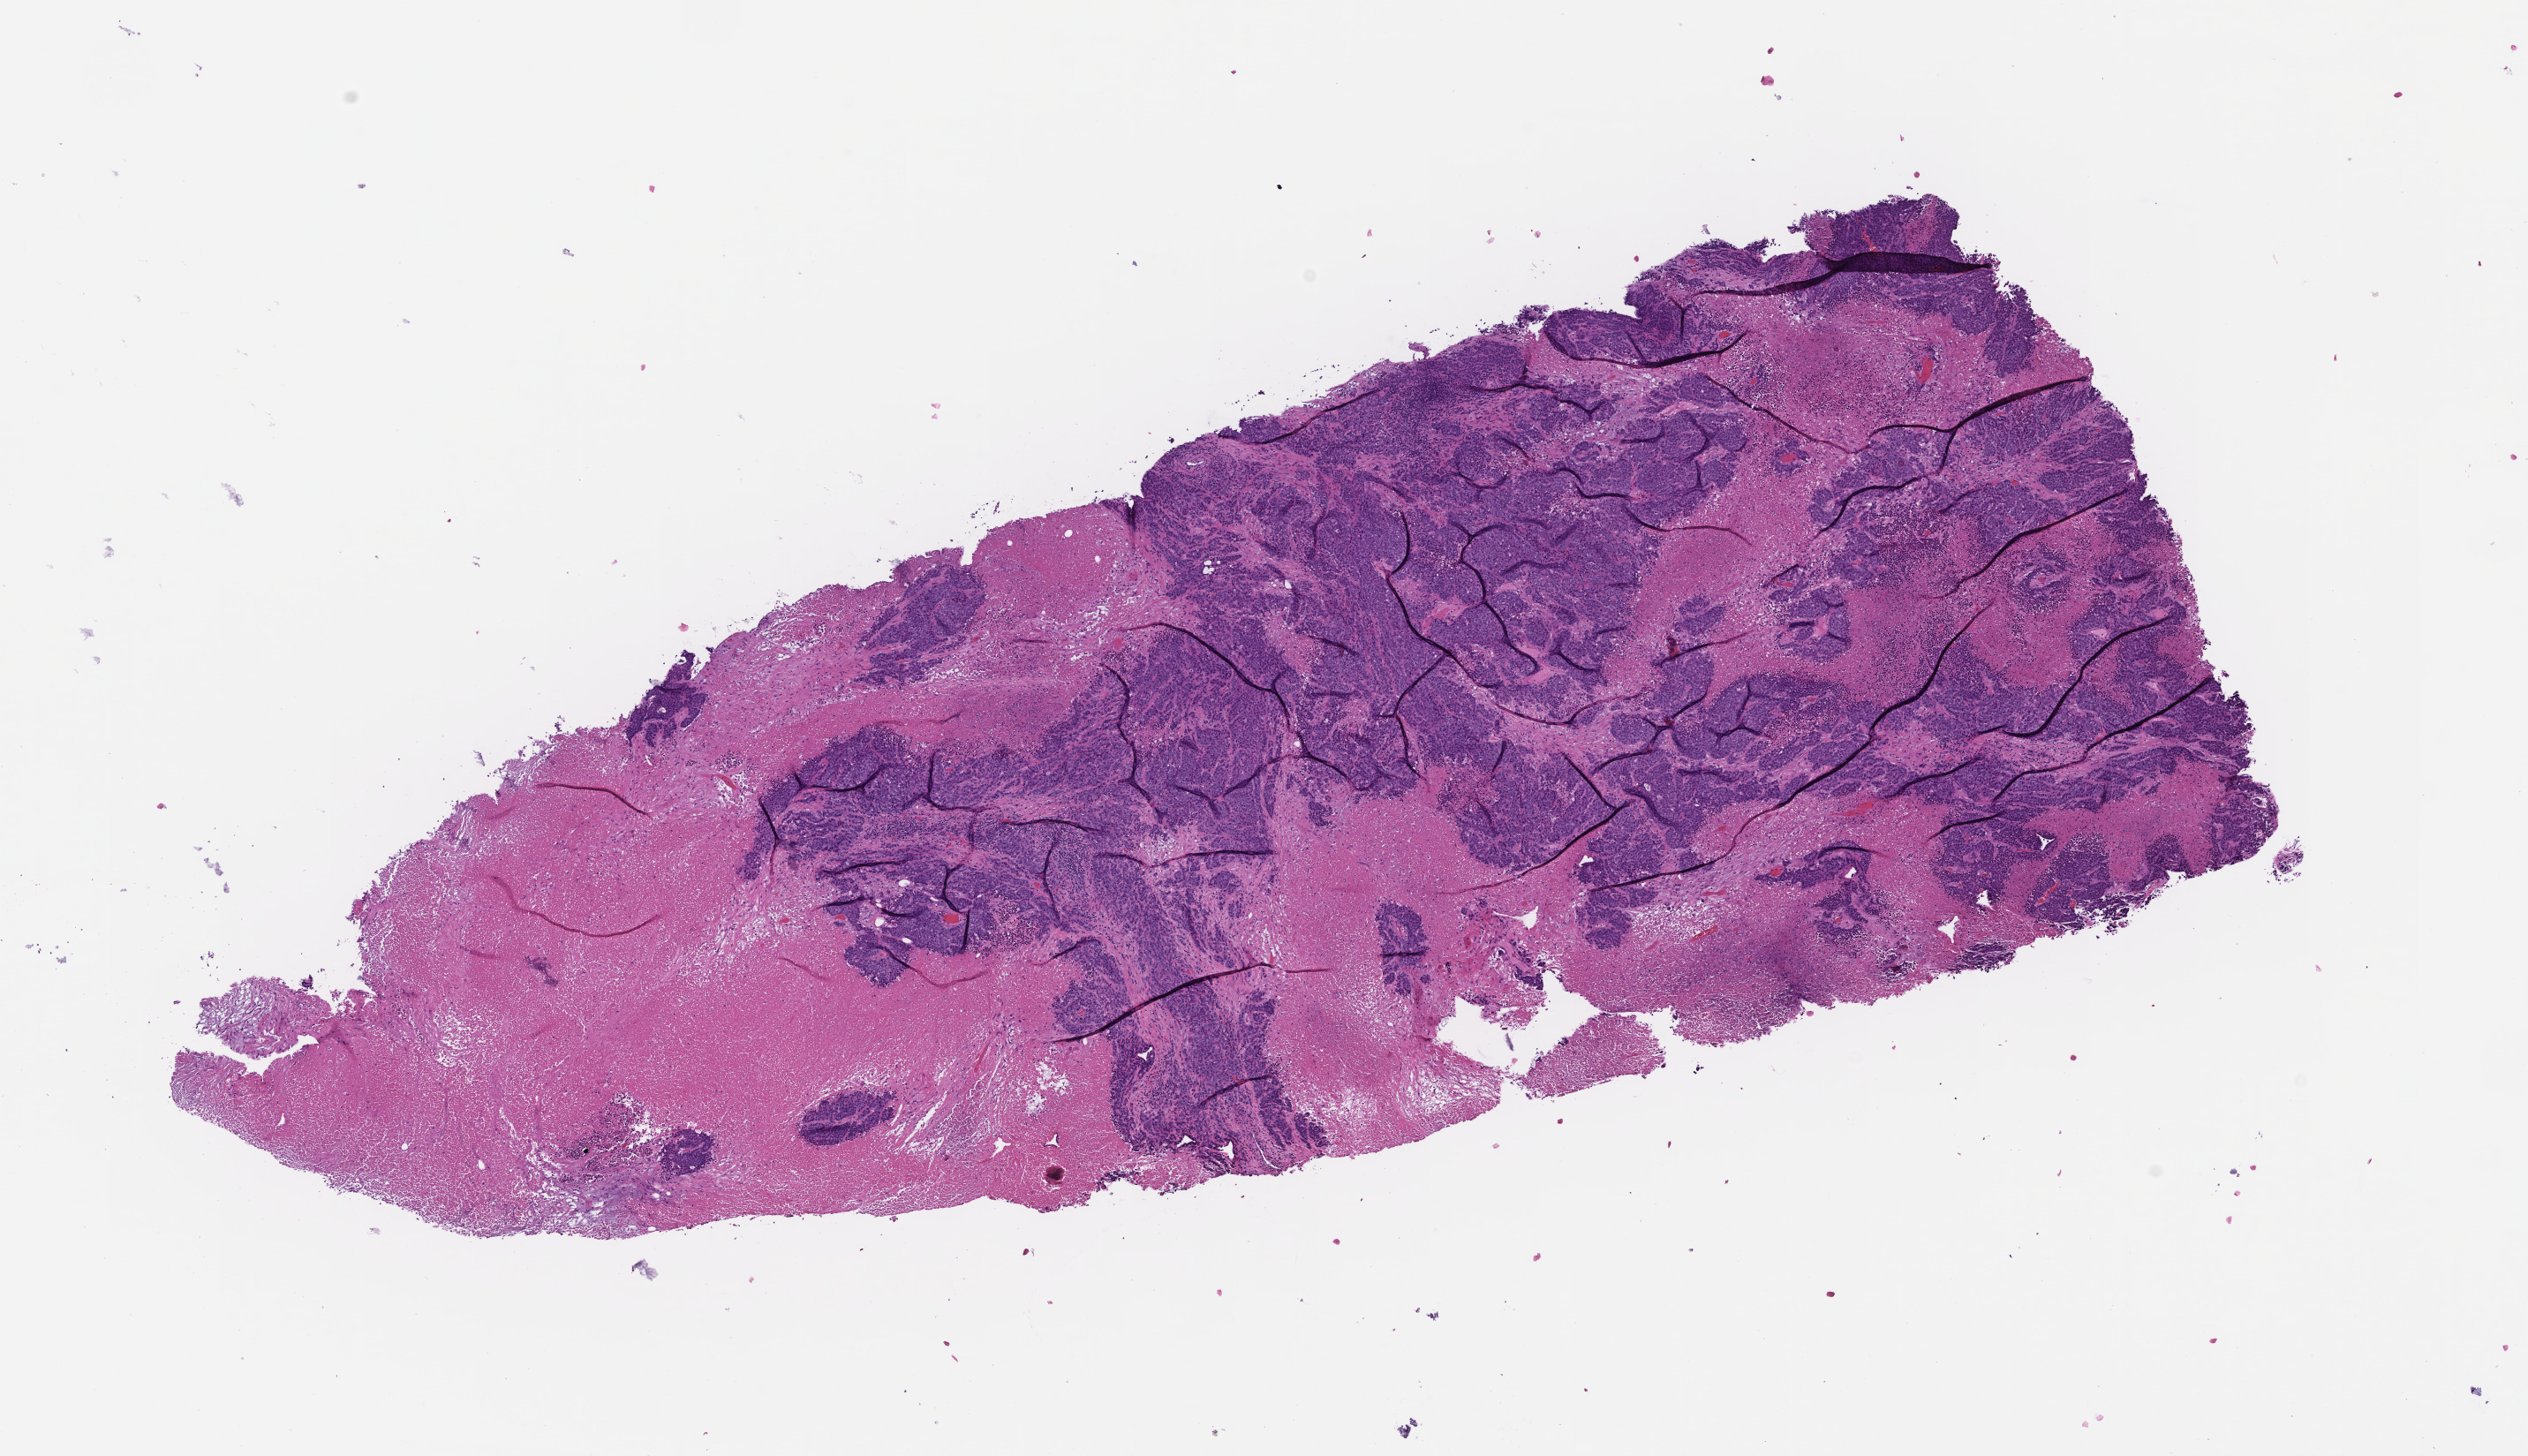
Whole-slide image, hematoxylin and eosin (H&E) stain — shown as a low-resolution overview of the whole scanned area (about 11.6 x 6.7 mm), FFPE section, specimen time point: collected at baseline (before treatment). Patient: female.
- this section: metastasis (sampled organ not recorded)
- patient diagnosis (primary): Colorectal Carcinoma